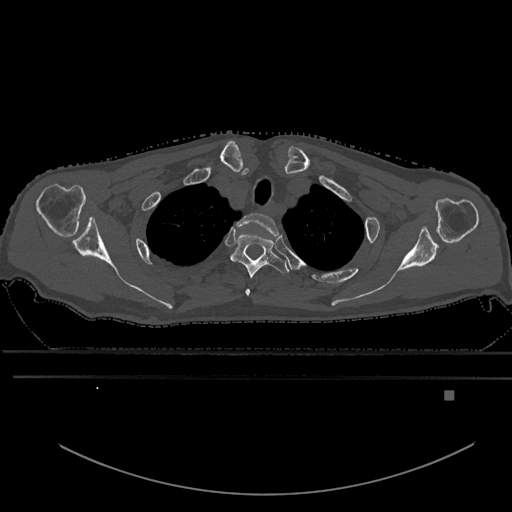
CT including the spine, one axial slice; position 501 of 969 along the scan axis; bone window (W 1800 / L 400 HU); 0.5 mm slice thickness; 512 × 512 image matrix, field of view 456 × 456 mm. Male patient, age 82 years. Case-level facts recorded for this patient, not image findings: primary cancer: prostate.
Annotated regions visible in this slice (semi-automatic segmentation, software-assisted and operator-edited):
- T1 vertebra: box from (x=236, y=212) to (x=279, y=235) px
- T2 vertebra: (x=231, y=233)–(x=289, y=295)